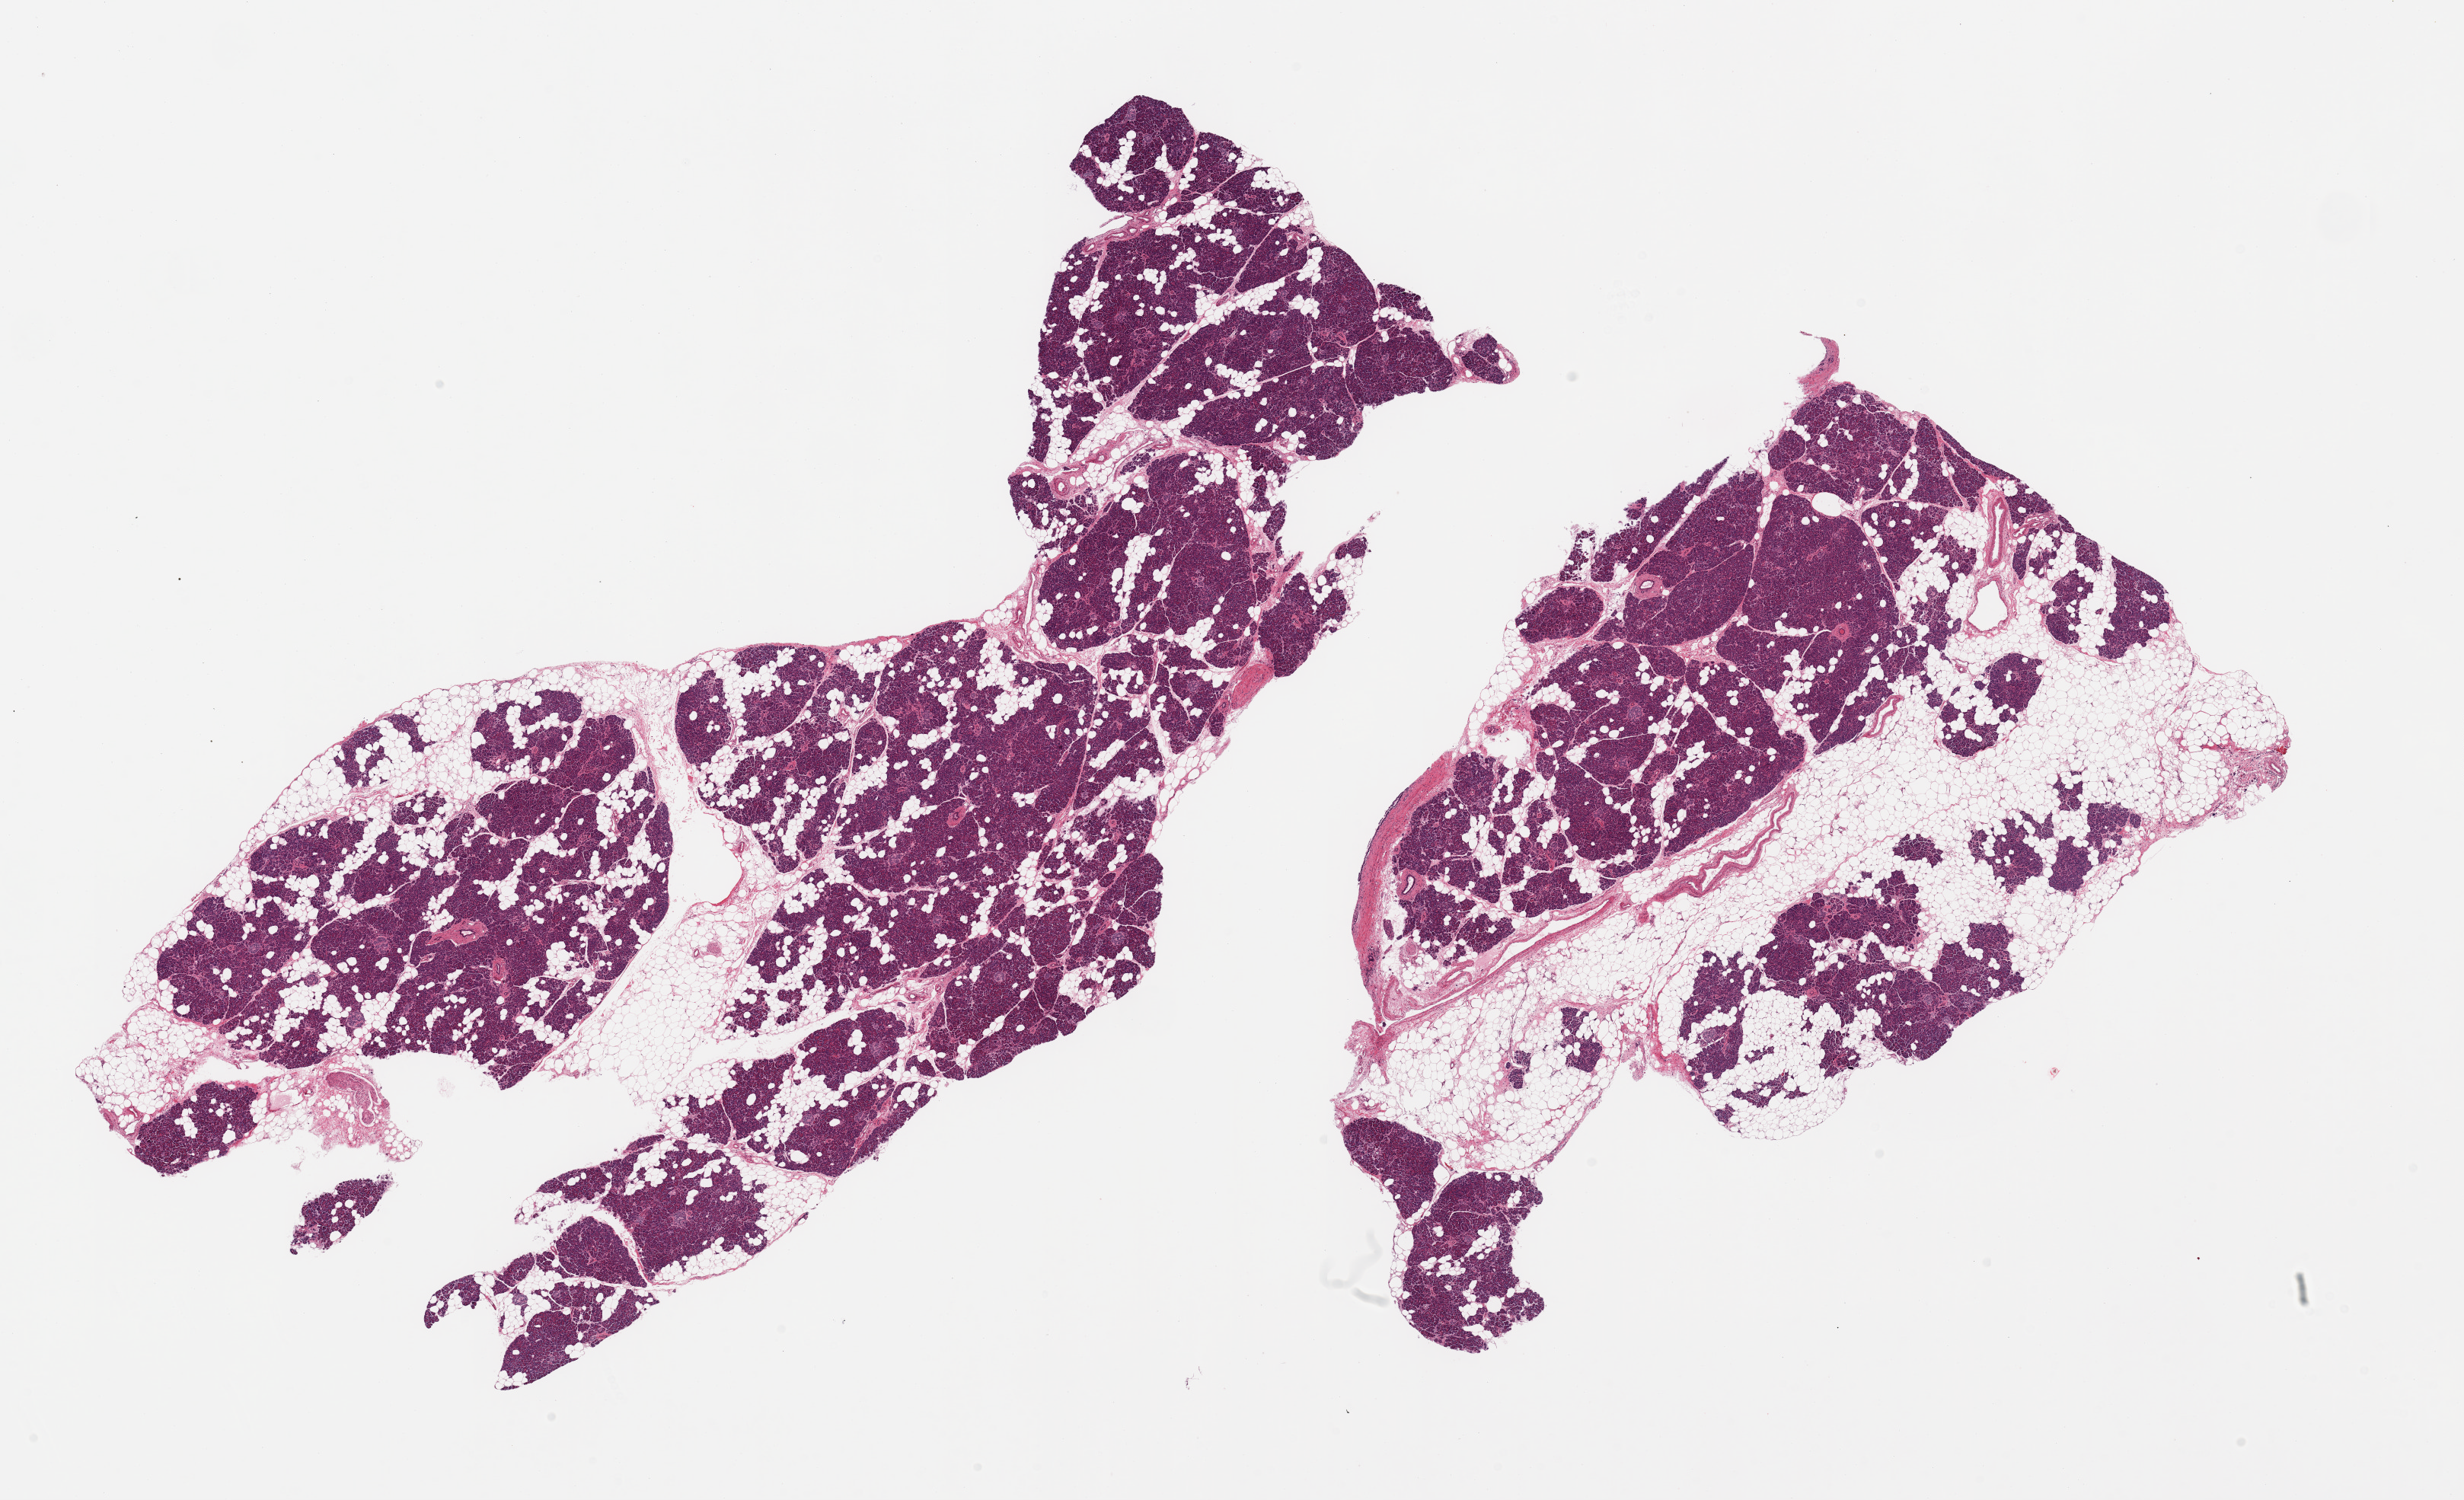
Whole-slide image, haematoxylin and eosin stain, a low-resolution overview of the entire scanned area, about 25.6 x 15.6 mm; PAXgene-fixed paraffin-embedded (PFPE) section; target tissue: pancreas; tissue donor sample. Donor sex: female.
Reviewer comment on this tissue sample: 2 pieces, ~40% interstitial/adherent fat; Islets rare but well -preserved.